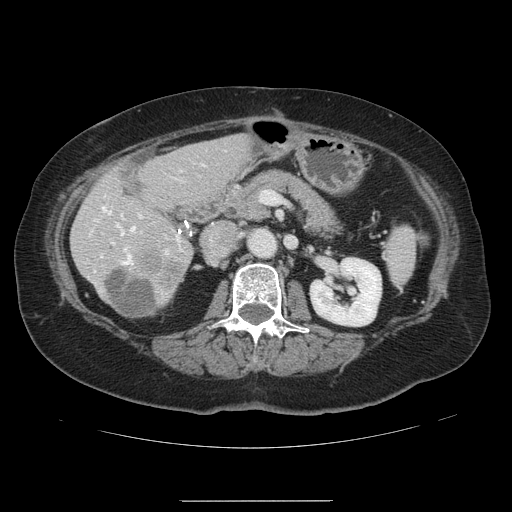
Contrast-enhanced abdominal CT, one axial slice. Position 56 of 141 along the scan axis. 120 kVp. Intravenous contrast given. Soft-tissue window (W 400 / L 40 HU). 2.5 mm slice thickness. 512 × 512 image matrix, field of view 393 × 393 mm. Female patient, age 74 years. Case-level facts recorded for this patient, not image findings: diagnosis: colorectal cancer liver metastases, imaged before liver resection; multiple liver metastases: yes; largest metastasis: 7 cm.
Outlined on this slice (expert manual segmentation):
- hepatic veins: box from (x=102, y=207) to (x=135, y=264) px
- liver: (x=72, y=136)–(x=252, y=319)
- planned liver remnant (the part of the liver to remain after resection): (x=81, y=136)–(x=252, y=319)
- portal vein (with intrahepatic branches): (x=111, y=163)–(x=204, y=253)
- liver metastasis: (x=109, y=271)–(x=159, y=315)
- liver metastasis: (x=140, y=253)–(x=186, y=289)